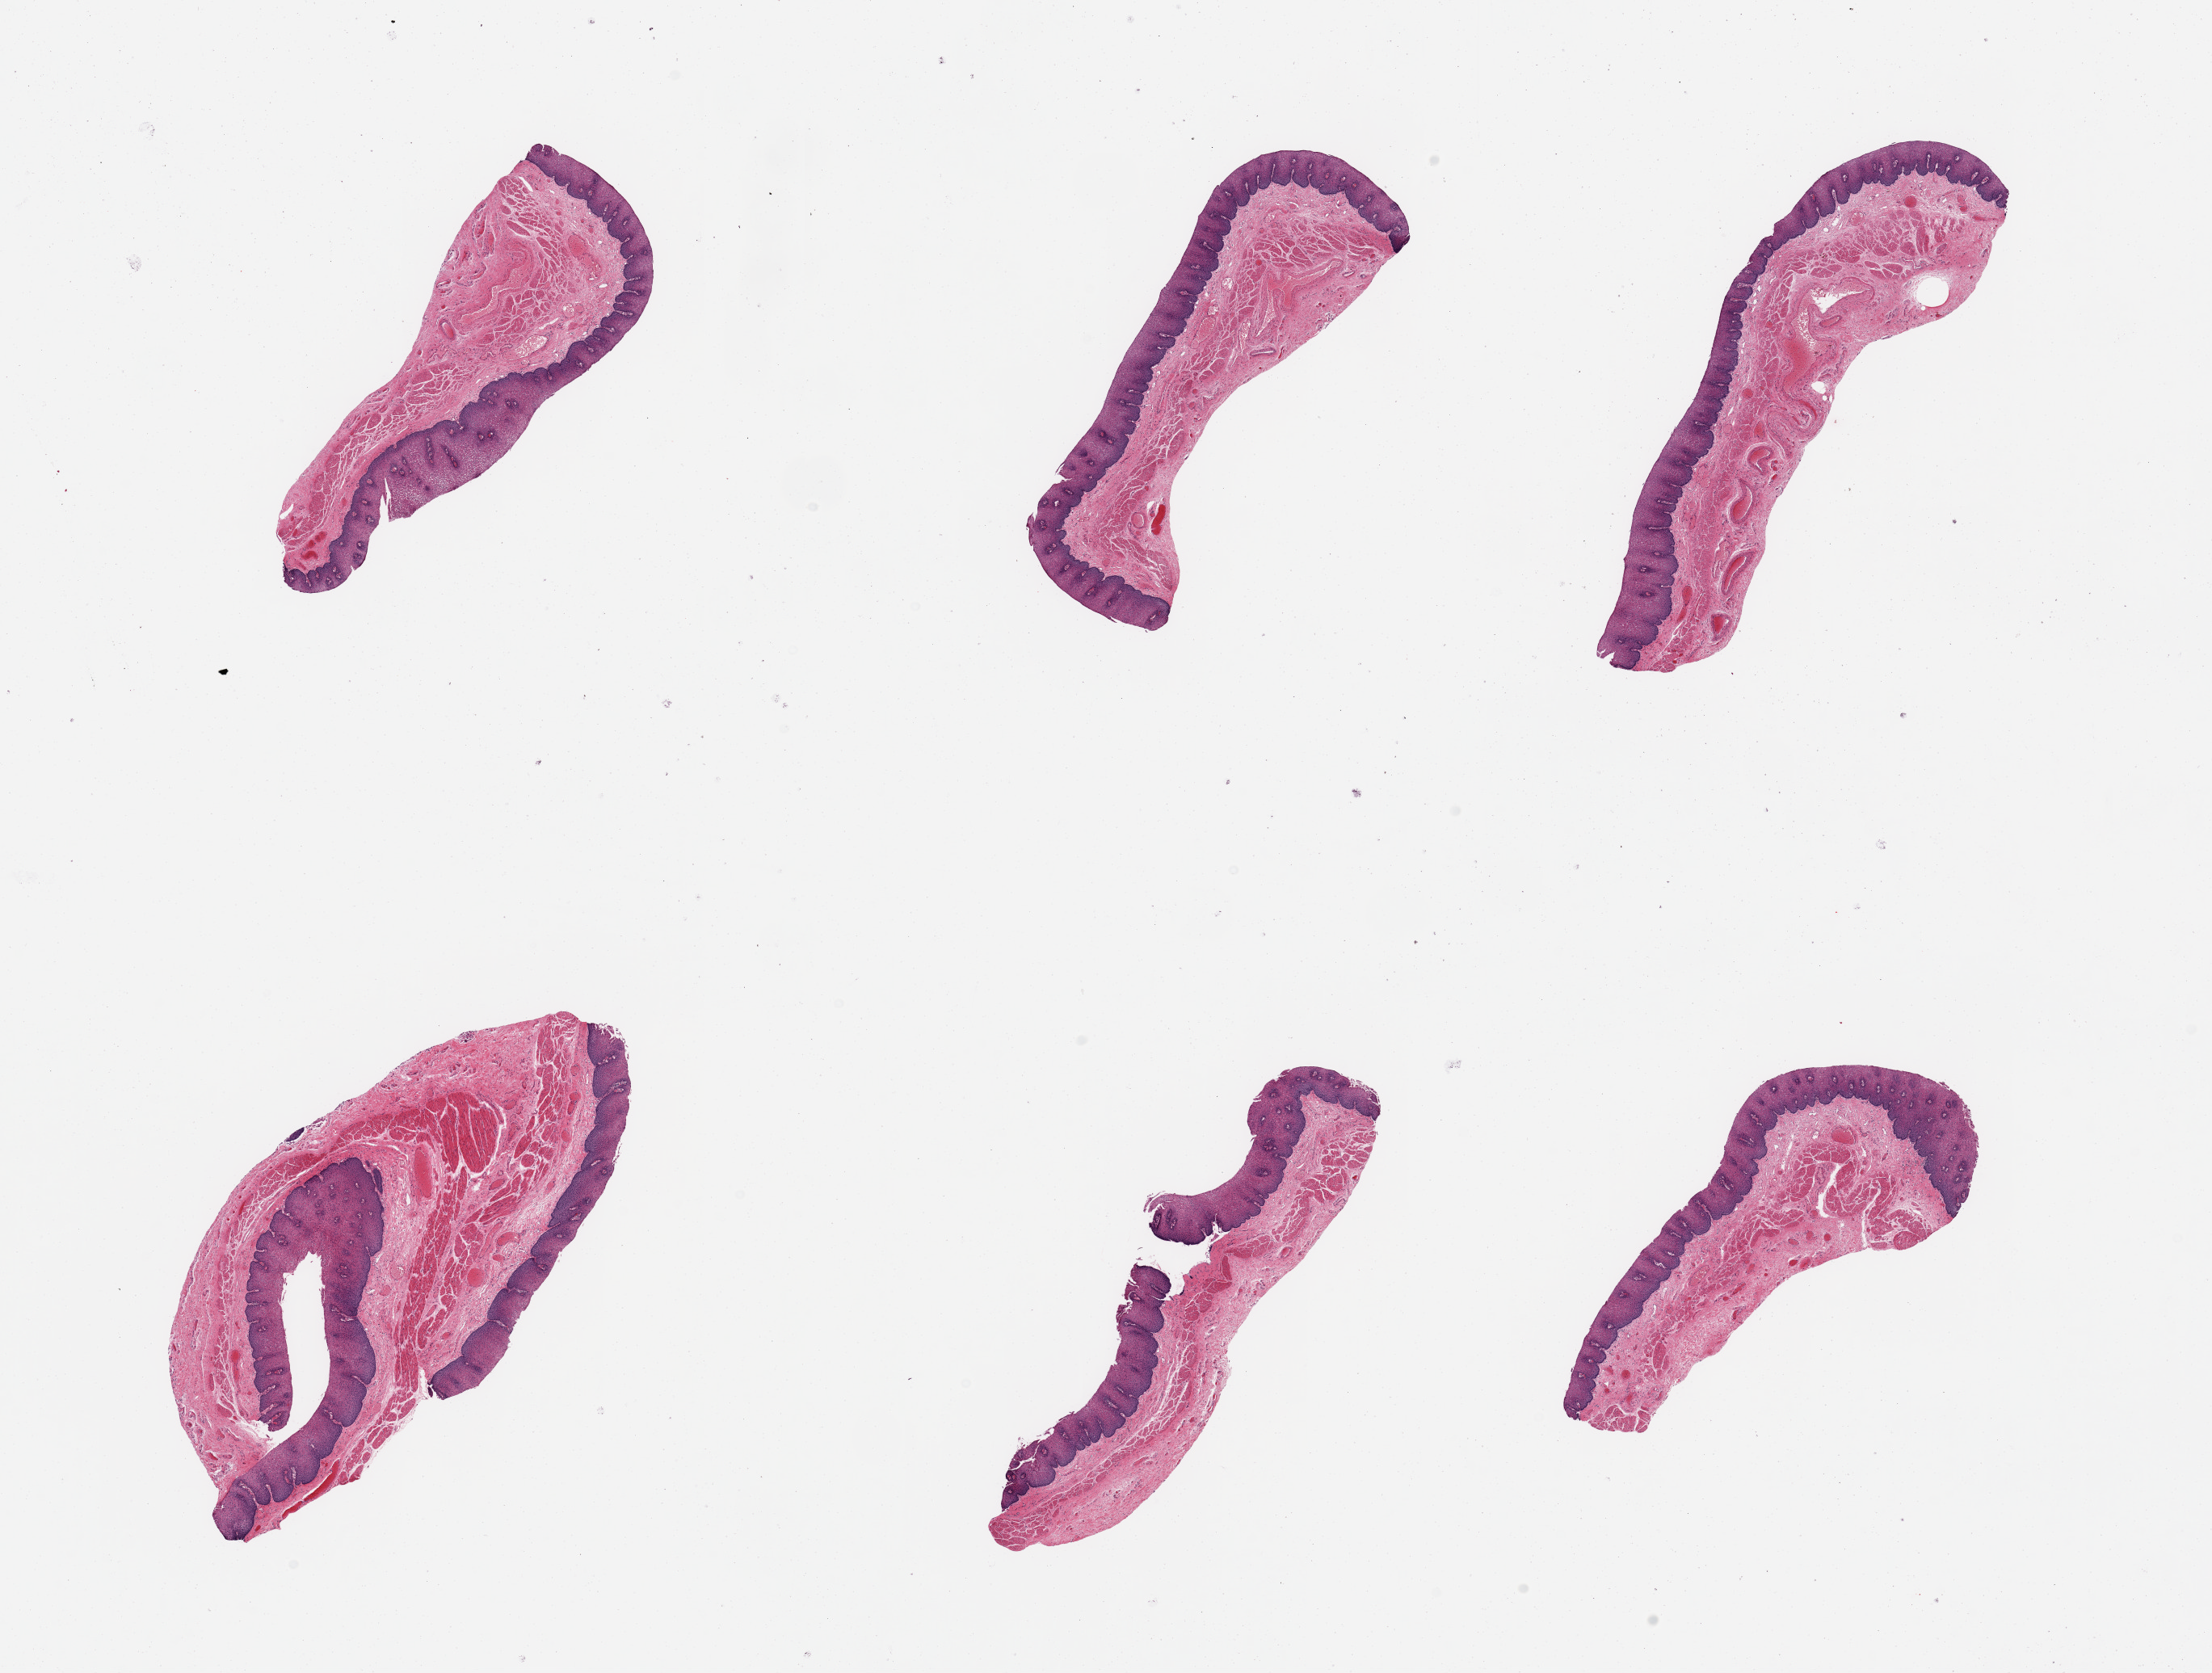
Haematoxylin and eosin whole-slide image — low-resolution overview of the scanned area, about 21.7 x 16.4 mm (from a 20x scan); PAXgene-fixed, paraffin-embedded tissue; target tissue: esophageal mucous membrane; tissue donor sample.
Review note (as recorded): 6 pieces; well preserved stratified squamous epithelium ~0.4um thick and muscularis mucosae.